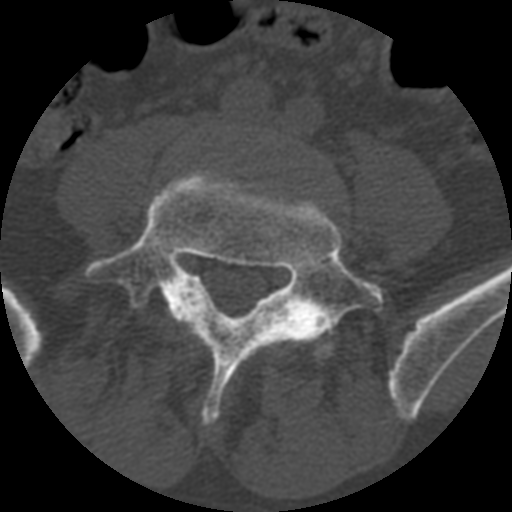
CT including the spine, one axial slice; position 260 of 399 along the scan axis; reconstruction kernel STANDARD; 120 kVp; bone window (W 1800 / L 400 HU); 1.25 mm slice thickness; 512 × 512 image matrix, field of view 160 × 160 mm. Patient age 71 years. From the clinical record (not read from this slice): primary cancer: prostate.
Annotated regions visible in this slice (semi-automatic segmentation, software-assisted and operator-edited):
- L4 vertebra: bounding box (x1, y1, x2, y2) in pixels: (179, 297, 195, 319)
- L5 vertebra: (84, 169, 384, 426)